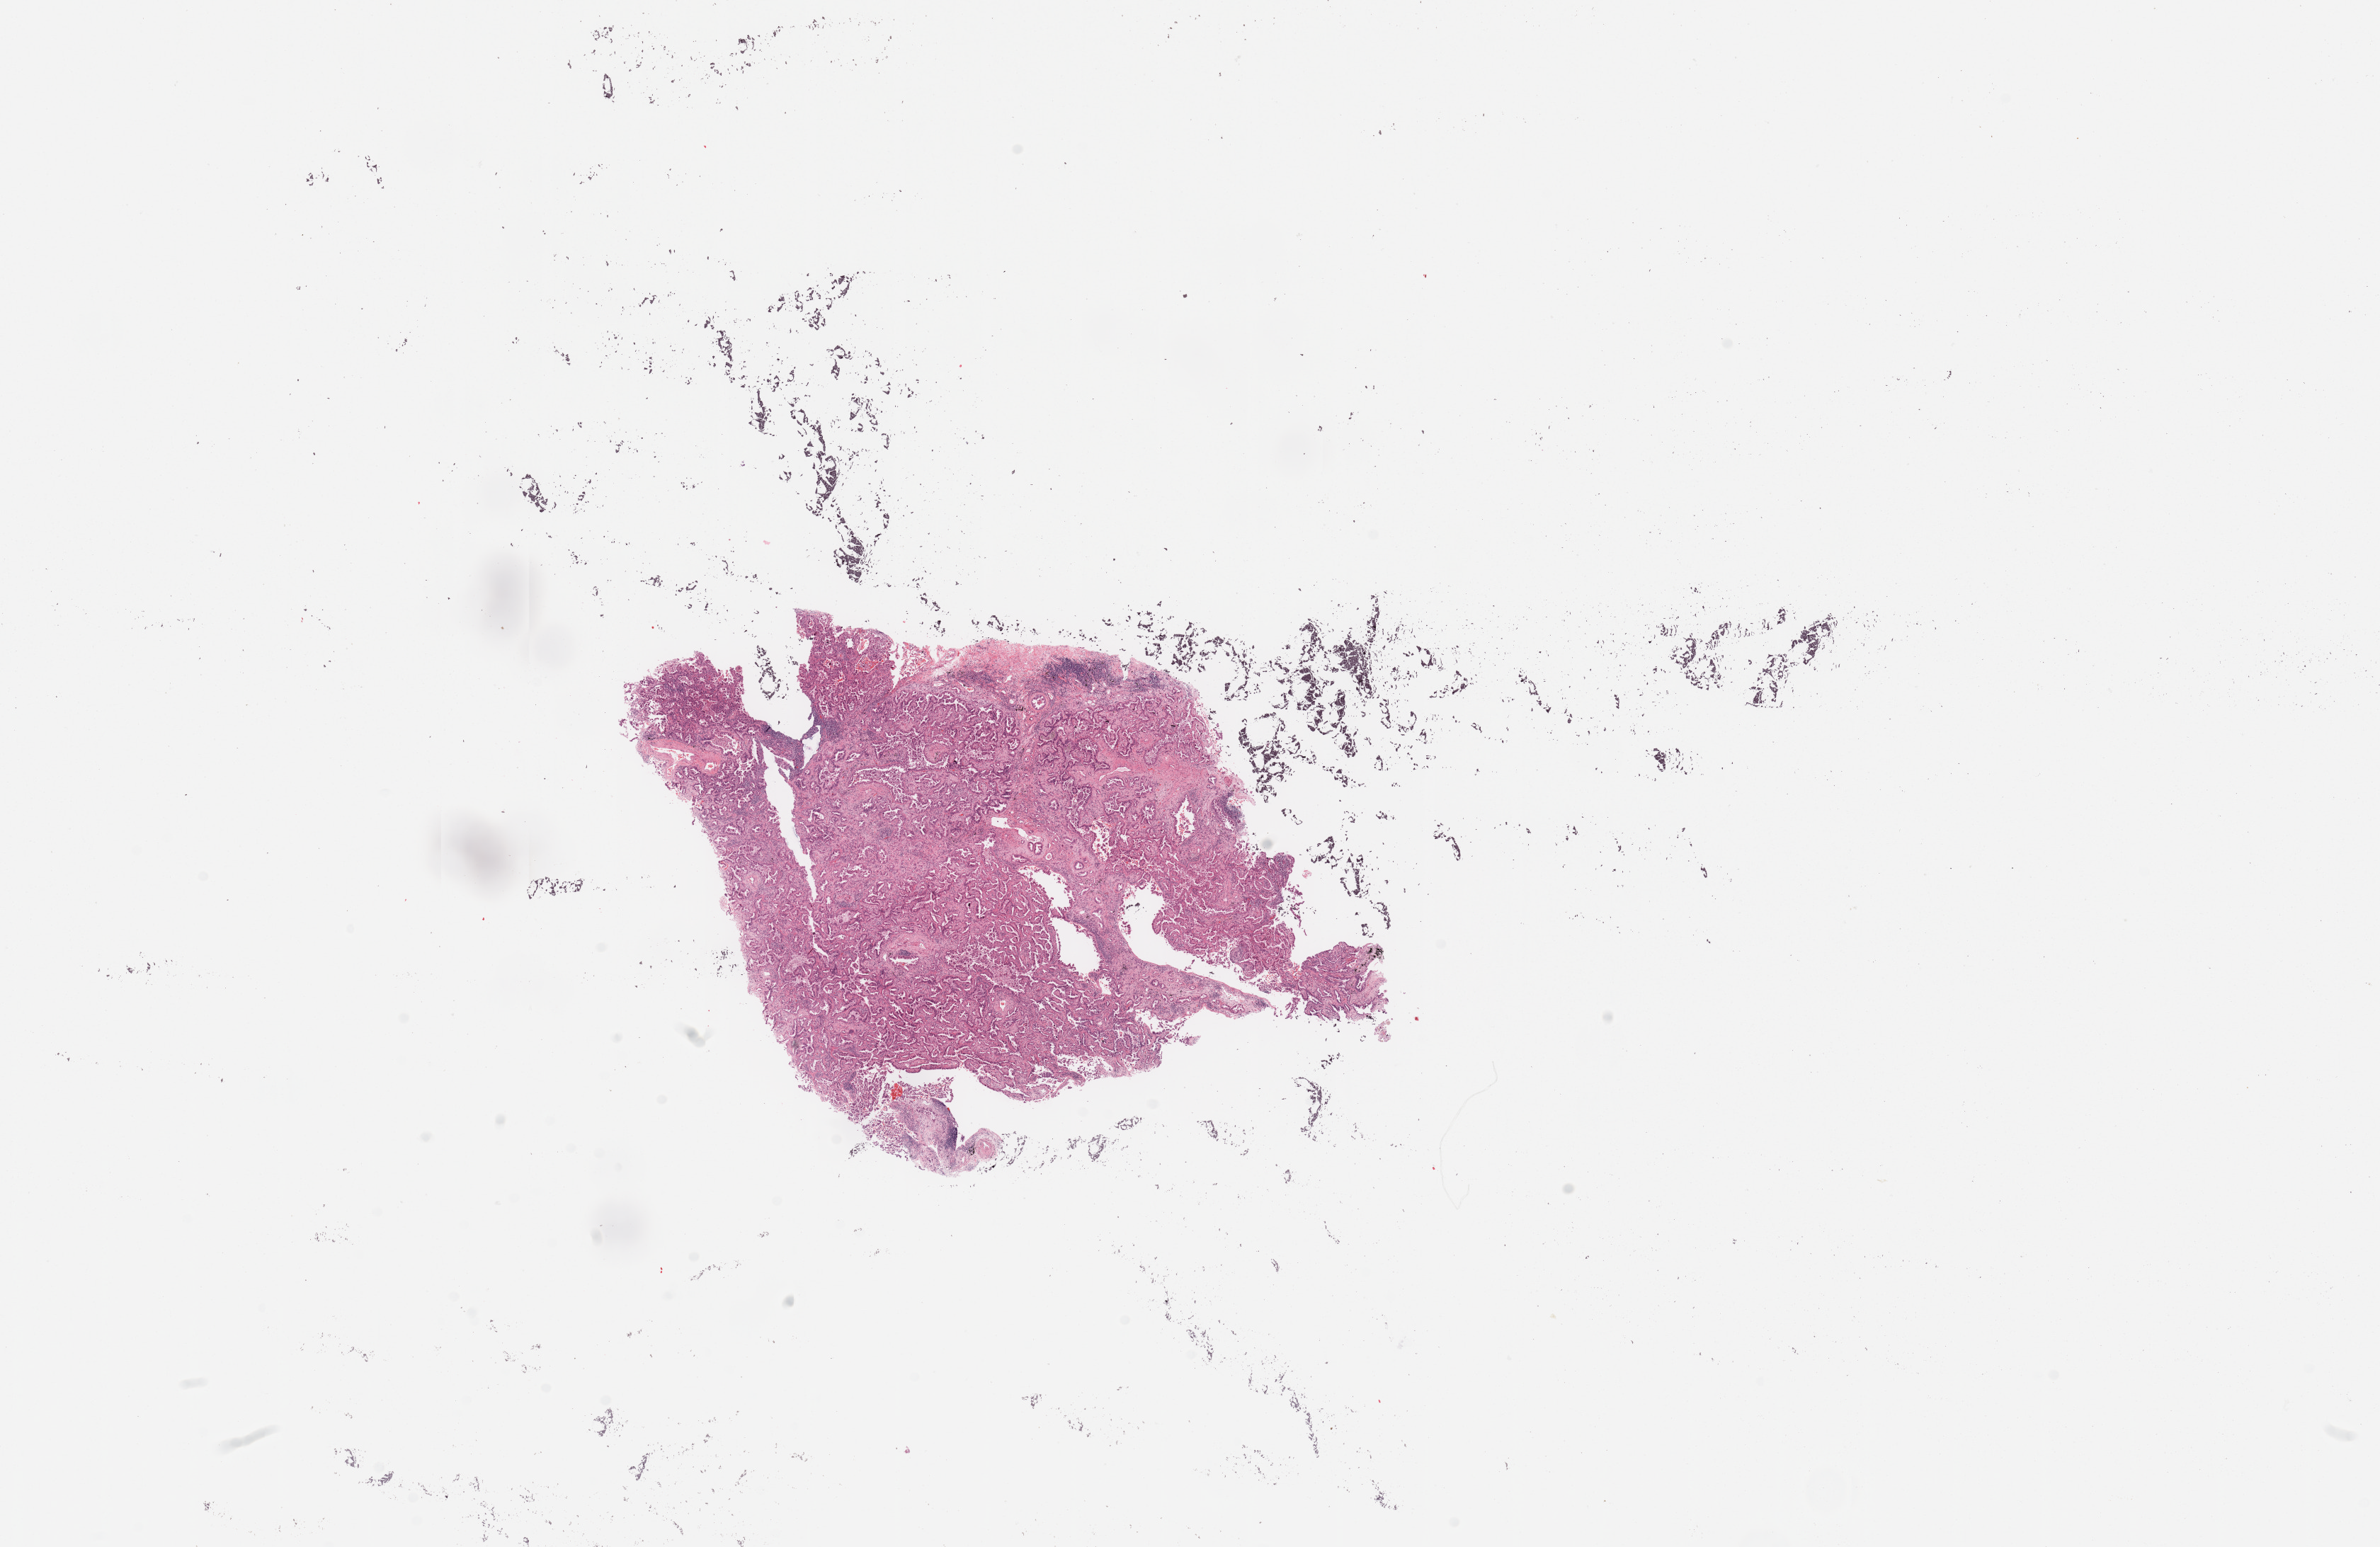
H&E whole-slide image — whole scanned area (about 26.6 x 17.3 mm, slide scanned at 20x) shown as a low-resolution overview, tumour tissue sample, sampled site: lung. 76-year-old female patient. Histologic grade: G2 (moderately differentiated). Slide review estimates, as recorded: tumour nuclei 75%, necrosis 3%.
Histologic diagnosis: Adenocarcinoma, NOS. AJCC pathologic stage: IIIA. Primary tumour site (as recorded): right lower lobe.